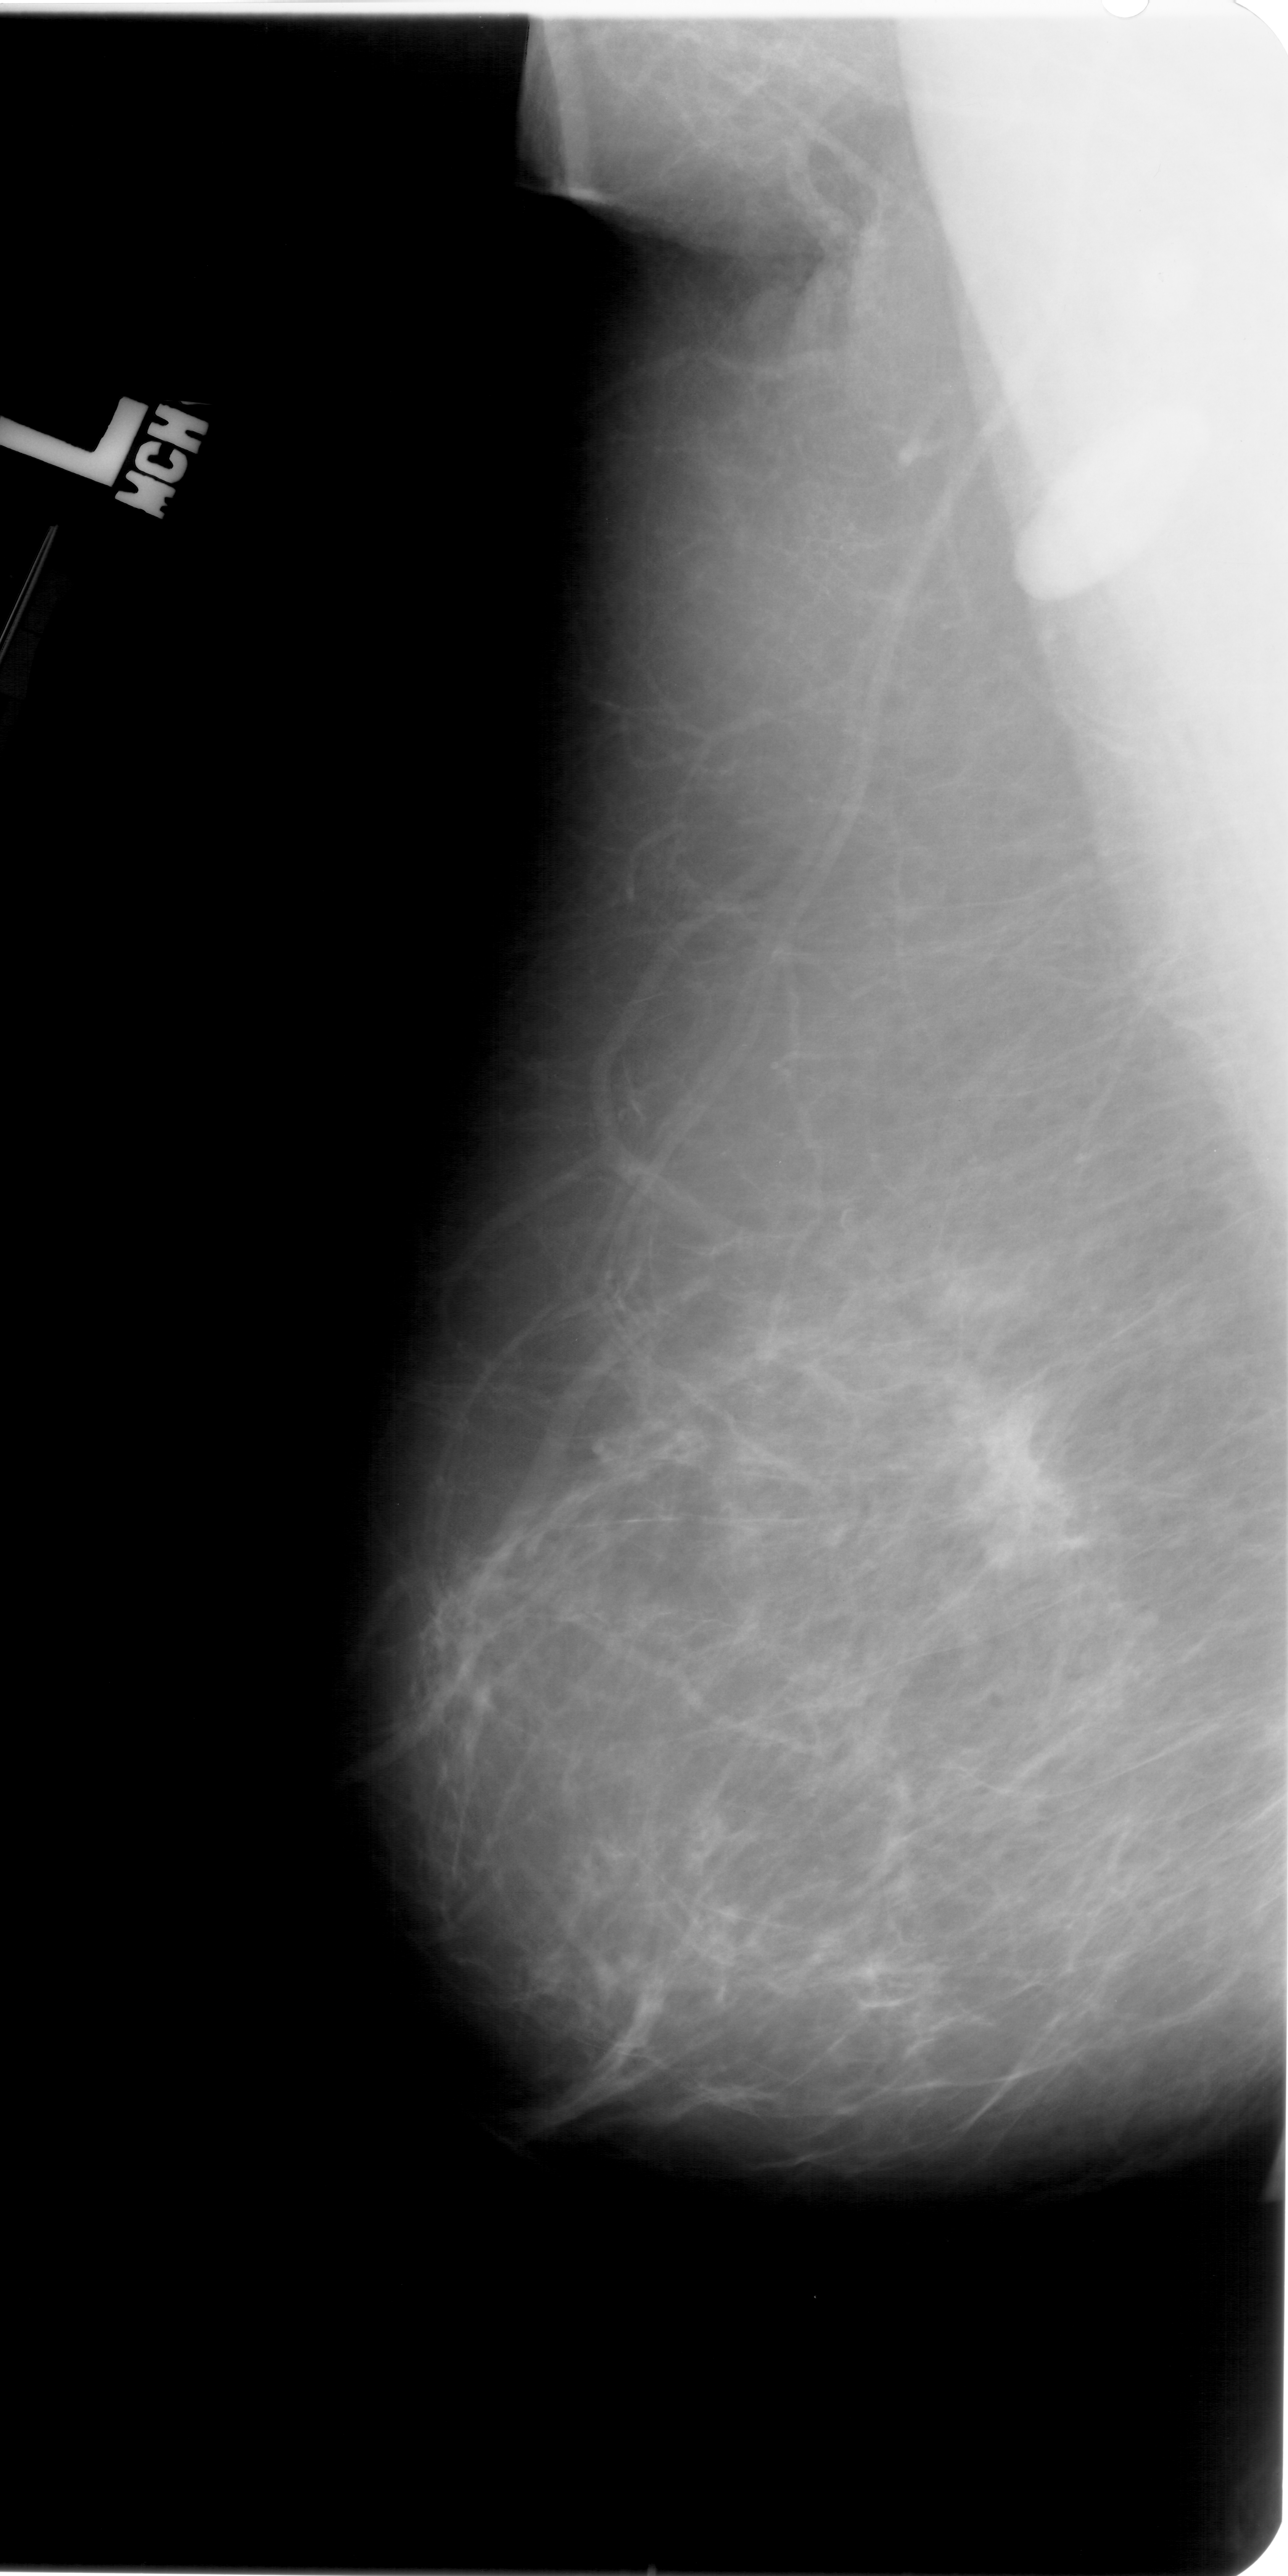
Digitized screen-film mammogram; left breast; MLO view; BI-RADS breast density category 2 (scale 1–4); 1288 × 2576 image matrix.
Marked abnormalities (boxes around the expert regions of interest):
- mass, shape irregular, margins spiculated; BI-RADS assessment category 5; pathology (as recorded): malignant: bounding box <964,1406,1092,1547> (left, top, right, bottom; pixels)